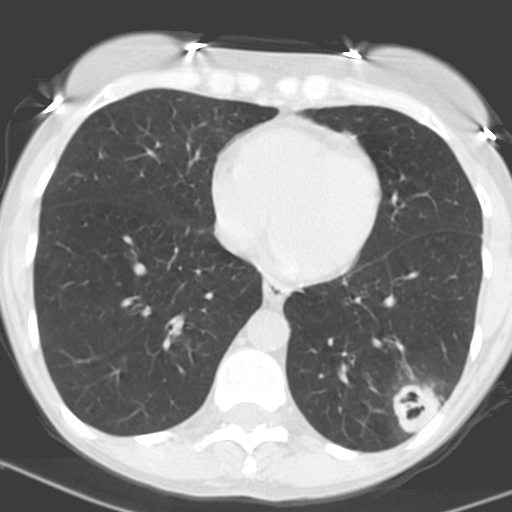
Chest CT (low-dose screening protocol), one axial image, baseline screening round, lung window (W 1500 / L -600 HU), 3.2 mm slice thickness, standard (soft-tissue) reconstruction kernel (C), slice 99 of 156 in the series. Female participant, aged 56 years at enrolment.
Lesion marked by an expert reader, bounding box [x1, y1, x2, y2] px = [373, 365, 454, 437]. Screening reader's record for this exam (one nodule recorded; not confirmed to be the boxed lesion): non-calcified nodule or mass ≥4 mm, left lower lobe, 31 × 23 mm, poorly defined margins, soft tissue attenuation, pre-existing on the prior screen: no. Official screen result: positive, change unspecified: nodule(s) >= 4 mm or enlarging nodule(s), mass(es), or other non-specific abnormalities suspicious for lung cancer. Lung cancer was diagnosed 27 days after this screen: squamous cell carcinoma, NOS, left lower lobe, poorly differentiated (G3), stage IB (AJCC 6th edition), 35 mm at pathology.